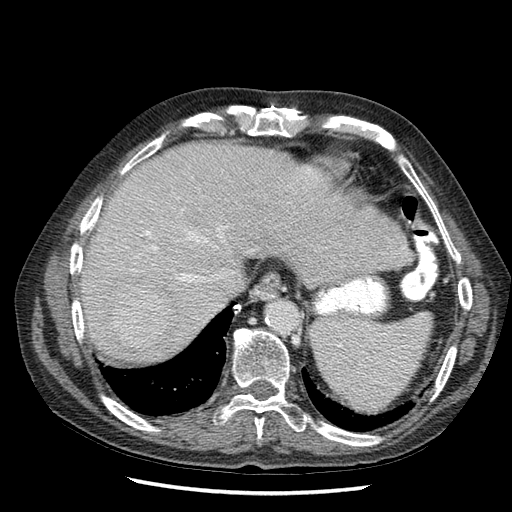
Contrast-enhanced abdominal CT (liver protocol), one axial slice; soft-tissue window (W 400 / L 40 HU); 512 × 512 image matrix. From the clinical record (not read from this slice): diagnosis: hepatocellular carcinoma (patient treated with transarterial chemoembolisation; whether this scan precedes or follows treatment is not stated here); TNM stage (as recorded): Stage-I; Child-Pugh class: A; tumour nodularity: uninodular.
Annotated regions visible in this slice (semi-automatic segmentation, software-assisted and operator-edited):
- liver parenchyma outside the tumour (the mass and vessels are separate outlines, so this box may not span the whole liver): bounding box (x1, y1, x2, y2) in pixels: (80, 140, 414, 364)
- mass: (111, 287, 172, 346)
- liver vessels: (146, 171, 312, 293)